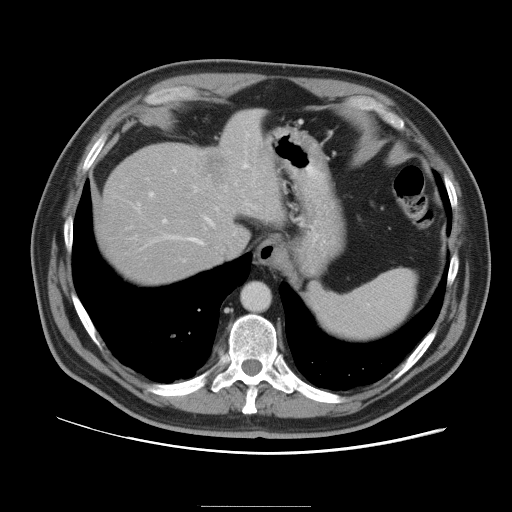
Contrast-enhanced abdominal CT, one axial slice; position 81 of 105 along the scan axis; intravenous contrast given; soft-tissue window (W 400 / L 40 HU); 5 mm slice thickness; 512 × 512 image matrix, field of view 399 × 399 mm. Male patient, age 64 years. From the clinical record (not read from this slice): diagnosis: colorectal cancer liver metastases, imaged before liver resection; multiple liver metastases: yes; largest metastasis: 3 cm; chemotherapy before resection: yes.
Structures marked on this image (expert manual segmentation):
- hepatic veins: bounding box <167,216,215,245> (left, top, right, bottom; pixels)
- liver: <99,111,280,284>
- planned liver remnant (the part of the liver to remain after resection): <98,150,230,283>
- portal vein (with intrahepatic branches): <149,164,248,224>
- liver metastasis: <205,152,228,184>